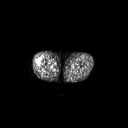
FDG PET of an extremity soft-tissue mass (from a PET/CT study), one axial slice. Position 223 of 267 along the scan axis. 3.27 mm slice thickness. 128 × 128 image matrix, field of view 700 × 700 mm. Male patient, age 43 years. Case-level facts recorded for this patient, not image findings: histological type: poorly differentiated synovial sarcoma; grade: high; site of the primary tumour: right buttock.
Structures marked on this image (expert contour drawn on MRI and transferred to this co-registered scan by the dataset authors):
- gross tumour volume including surrounding oedema: bounding box <35,59,43,67> (left, top, right, bottom; pixels)